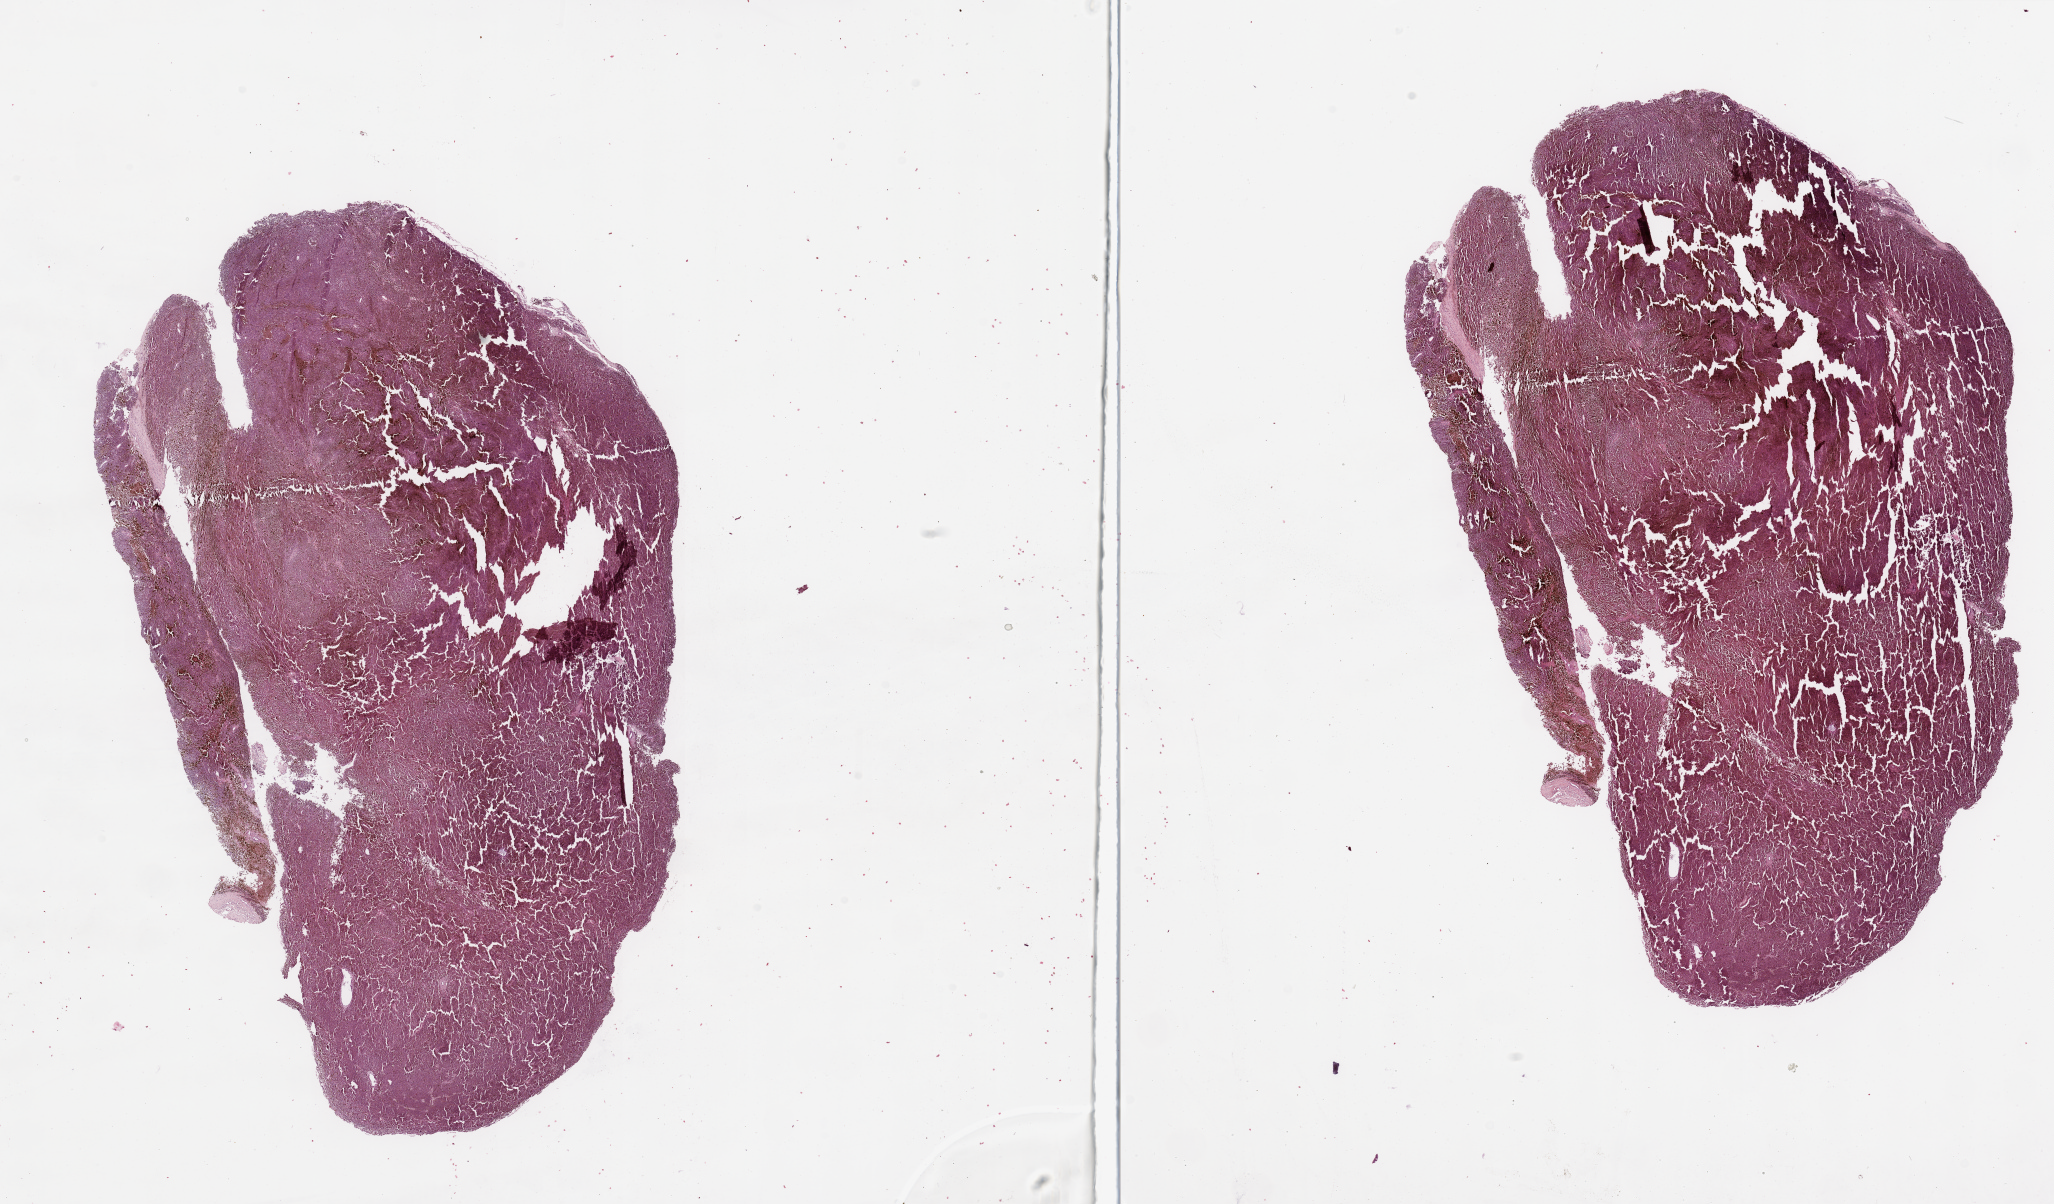
Digitized H&E-stained tissue section (whole slide) — a low-resolution overview of the entire scanned area, about 32.5 x 19.0 mm. Melanoma tumour tissue; sampled site not recorded. Female, 54 y/o.
Primary tumour site (as recorded): trunk. Diagnosis: Malignant melanoma, NOS. AJCC pathologic stage: IIA.